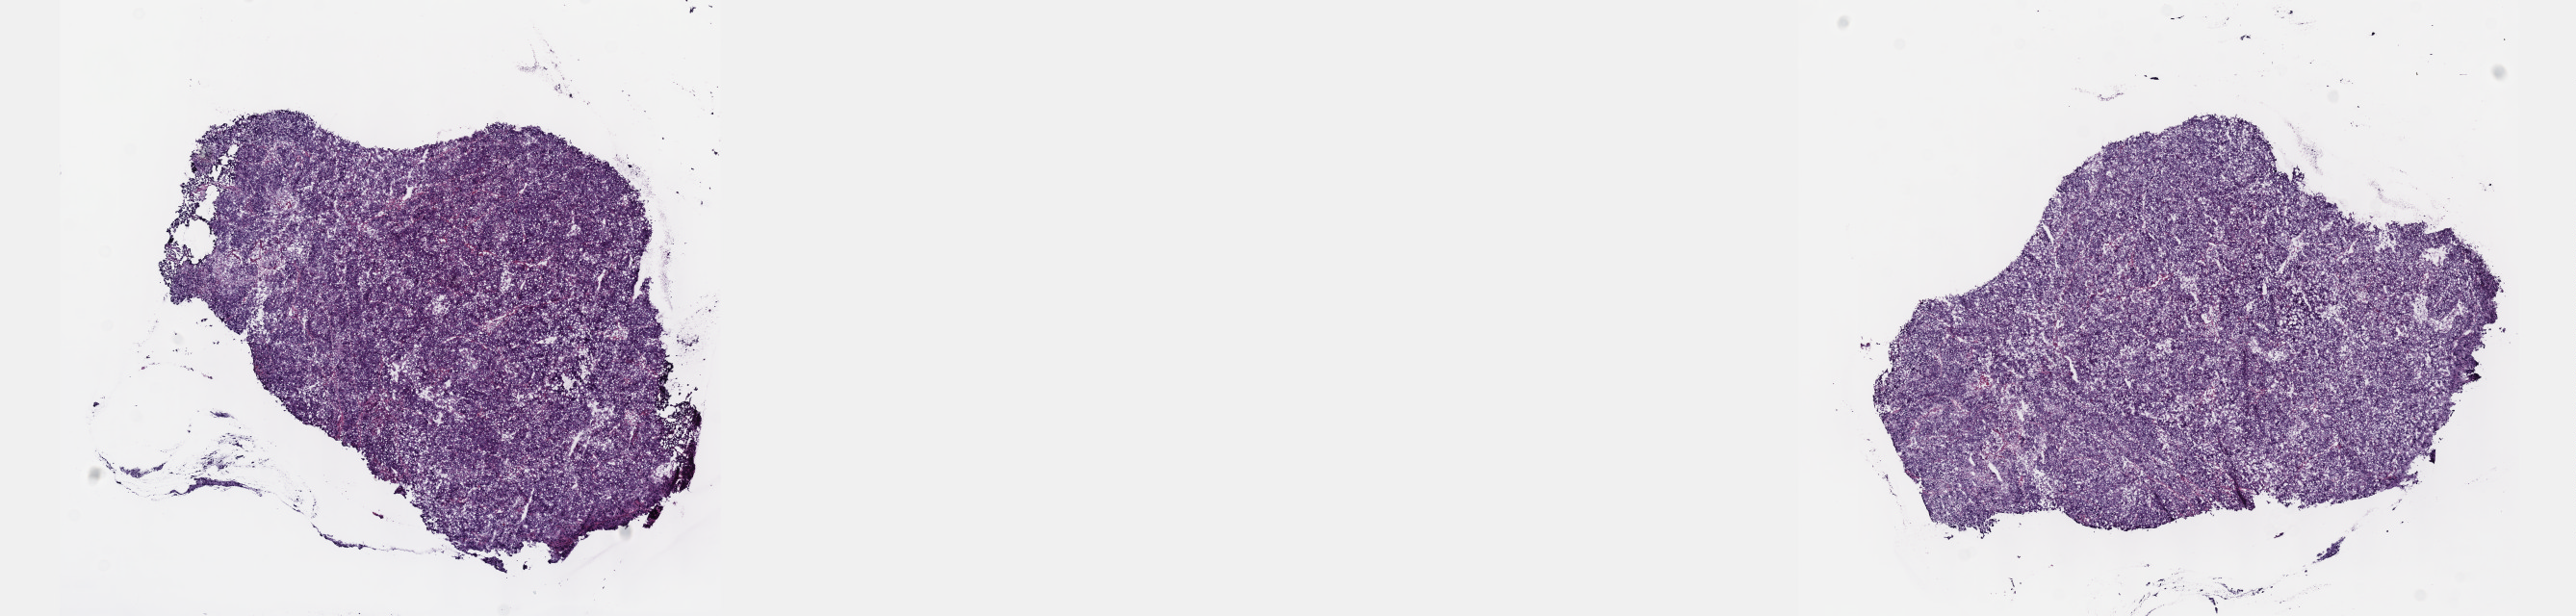
Hematoxylin and eosin (H&E) stained whole-slide image — whole scanned area (about 21.6 x 5.2 mm, from a 40x scan) shown as a low-resolution overview. Frozen section from the top of the tissue portion. Liver, primary tumour sample. Patient: male, age at initial diagnosis 59 years. Histologic grade: G4 (undifferentiated). Composition of this section per pathologist review: tumour cells 90%, tumour nuclei 95%, normal cells 0%, stromal cells 10%, necrosis 0%. Infiltration values recorded for this section: lymphocyte infiltration 0%, monocyte infiltration 0%, neutrophil infiltration 0%.
AJCC pathologic stage: I. Pathologic diagnosis: Hepatocellular carcinoma, NOS.